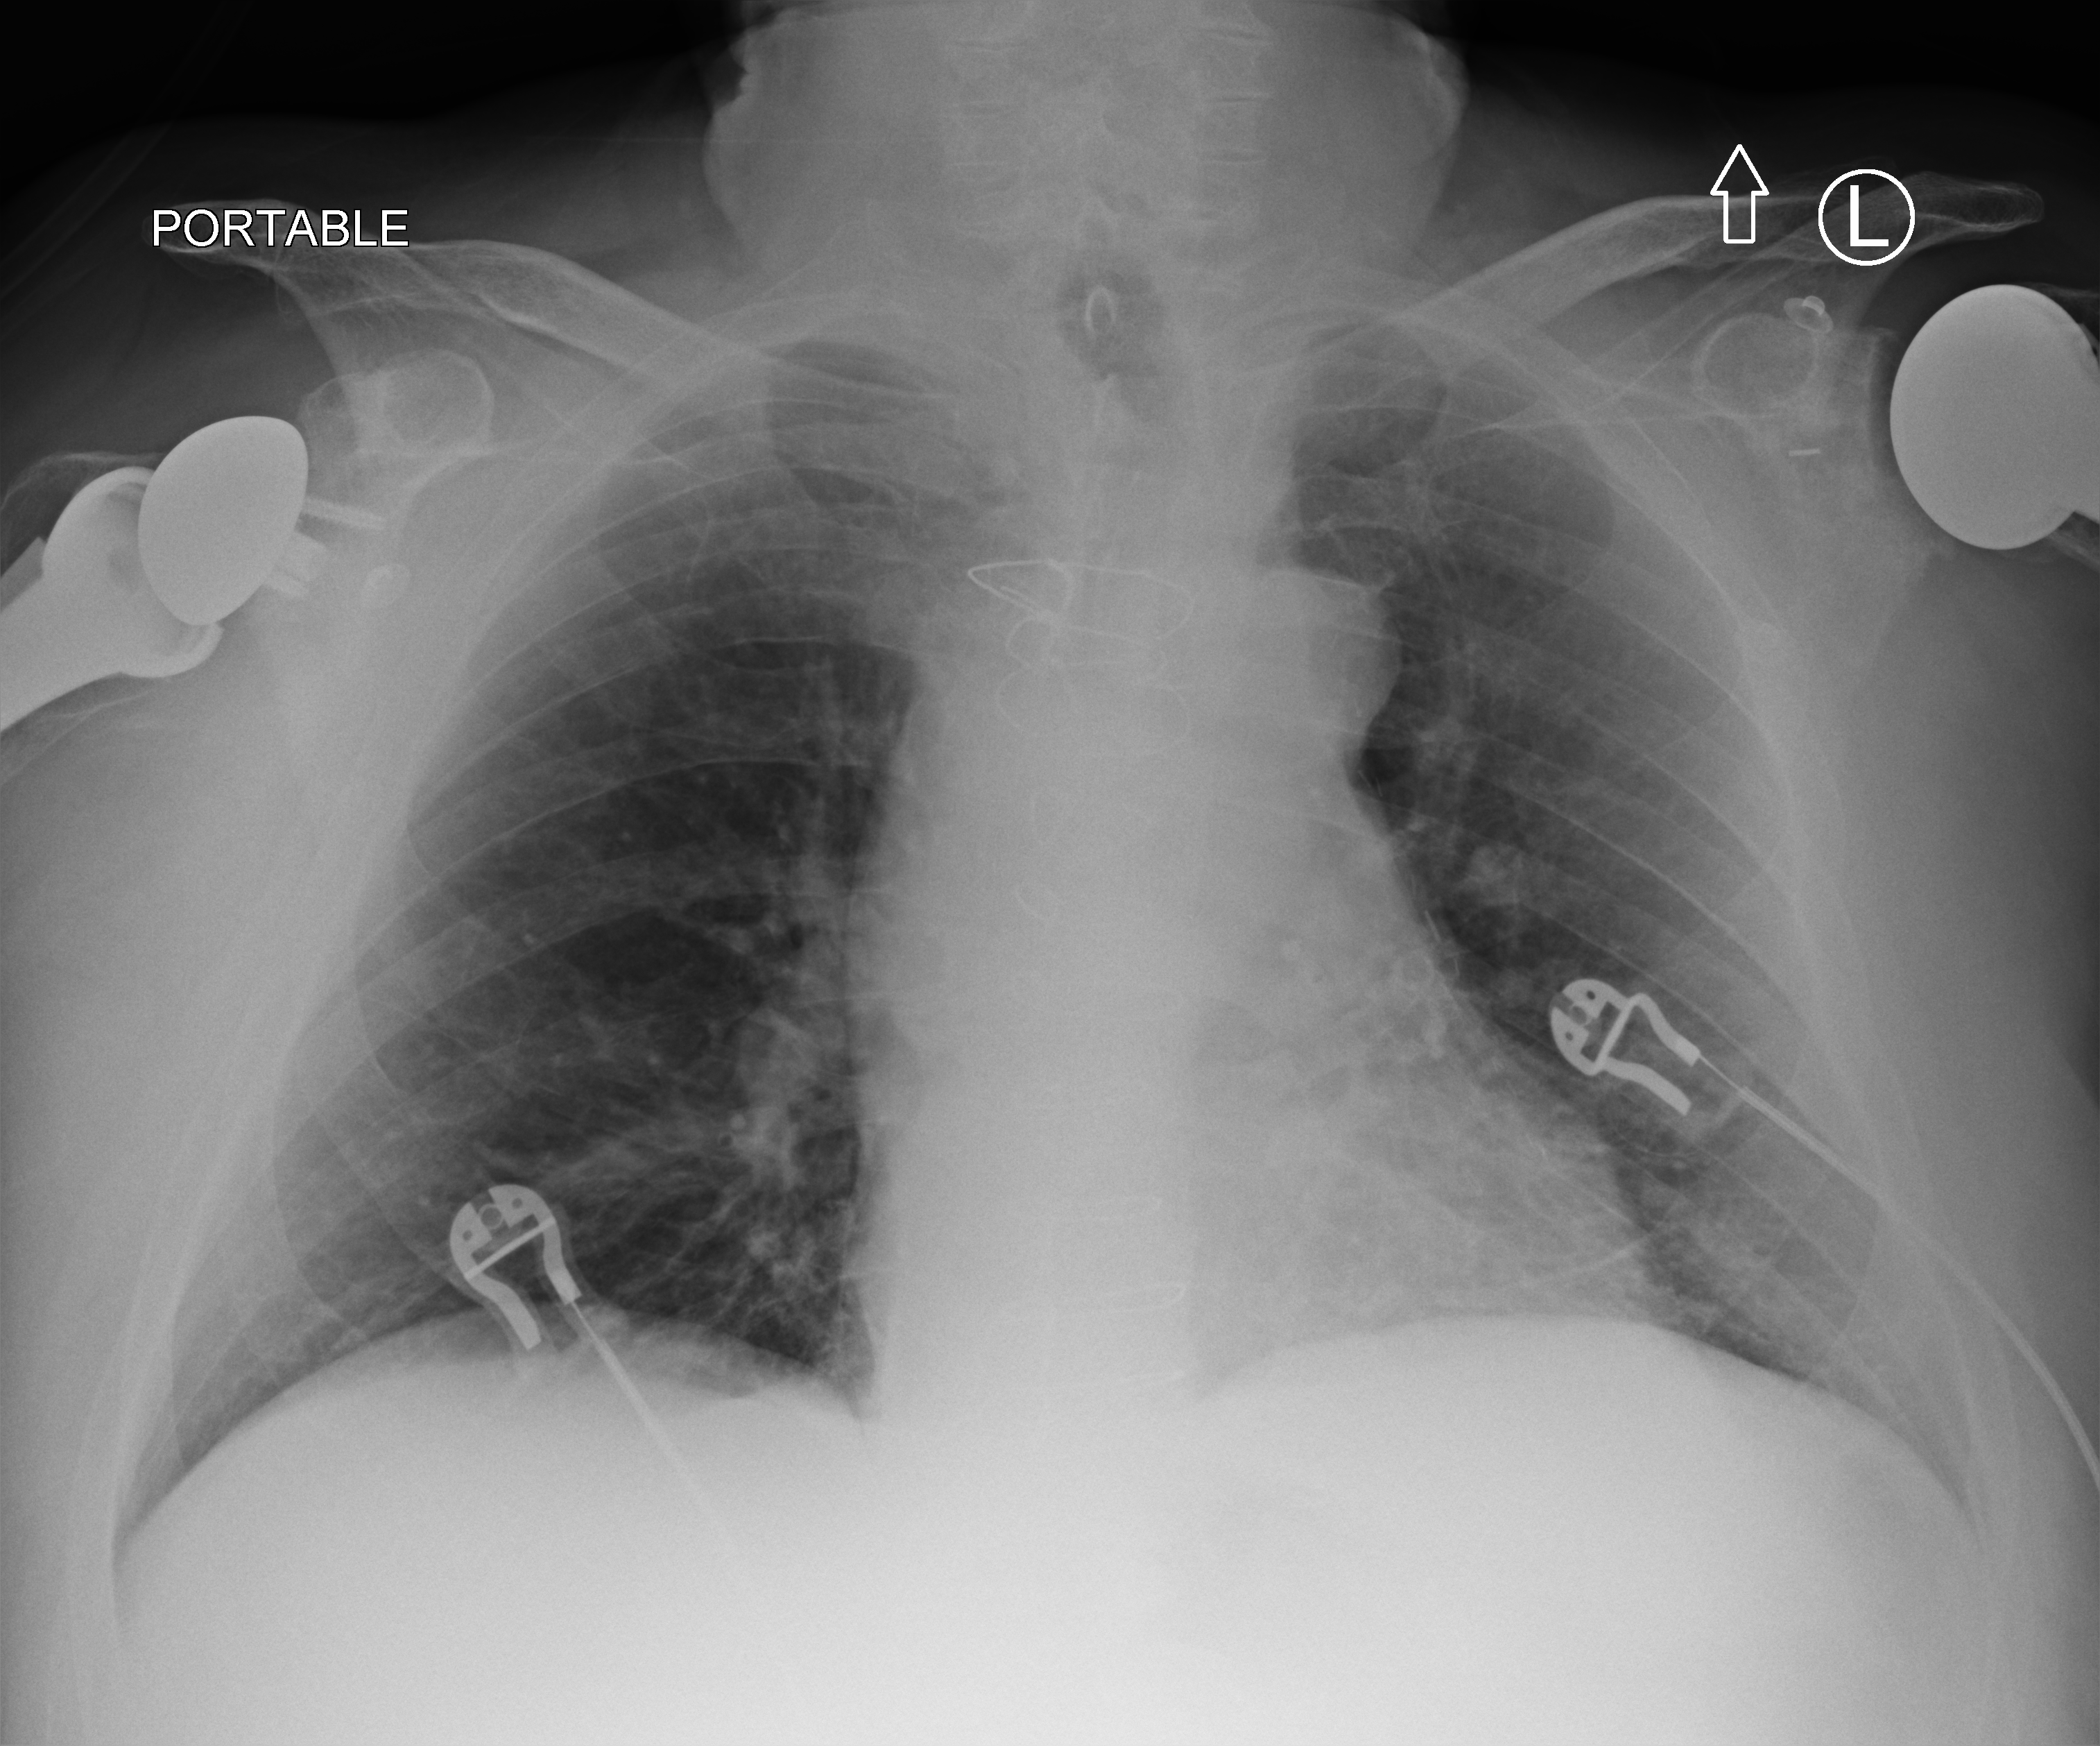
Chest X-ray (portable), anteroposterior (AP) projection. Patient hospitalised with COVID-19; male, aged 60–74 years.
Hospital-stay facts (about this admission, not read from this image; timing relative to this image not recorded): mechanically ventilated during this hospital stay: no; COPD (admission record): no; admitted to intensive care during this hospital stay: no.